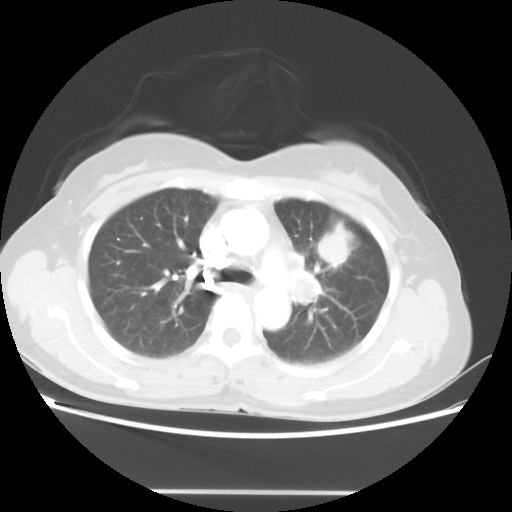
Chest CT, one axial slice; position 31 of 46 along the scan axis; reconstruction kernel STANDARD; 100 kVp; lung window (W 1500 / L -600 HU); 512 × 512 image matrix, field of view 360 × 360 mm. Female patient, age 50 years. Case-level facts recorded for this patient, not image findings: clinical TNM (as recorded): T1c N1 M0.
Structures marked on this image (rectangle marked by the reading radiologist):
- lung tumour (recorded histology: adenocarcinoma): bounding box (x1, y1, x2, y2) in pixels: (320, 225, 348, 267)